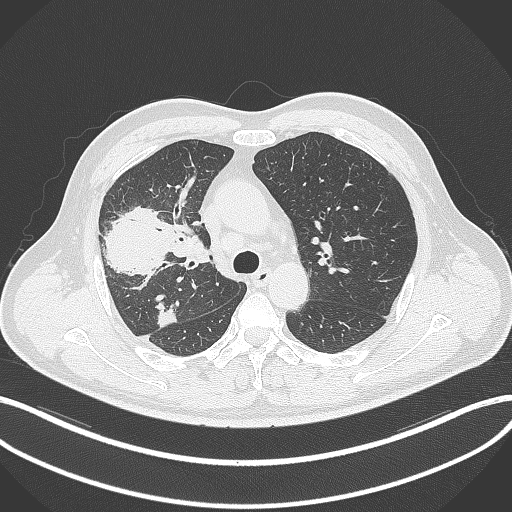
Chest CT, one axial slice; slice 227 of 348 in the series (ordered by position); reconstruction kernel B70f; 120 kVp; lung window (W 1500 / L -600 HU); 512 × 512 image matrix, field of view 400 × 400 mm. Patient: male, 55 years. Case-level facts recorded for this patient, not image findings: clinical TNM (as recorded): T3 N2 M1.
Annotated regions visible in this slice (bounding box drawn by a radiologist):
- lung tumour (recorded histology: adenocarcinoma): bounding box [x1, y1, x2, y2] px = [96, 204, 166, 279]